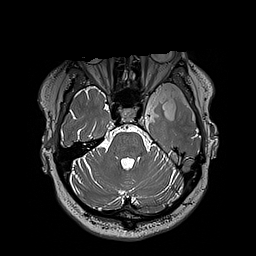
Brain MRI from a brain-tumour surgery series, one axial slice. Position 142 of 192 along the scan axis. 1 mm slice thickness. 256 × 256 image matrix, field of view 250 × 250 mm. From the clinical record (not read from this slice): histopathology: Oligodendroglioma; WHO grade: 3; IDH mutation: yes.
Outlined on this slice (expert manual segmentation):
- tumour: bounding box (x1, y1, x2, y2) in pixels: (153, 82, 195, 119)